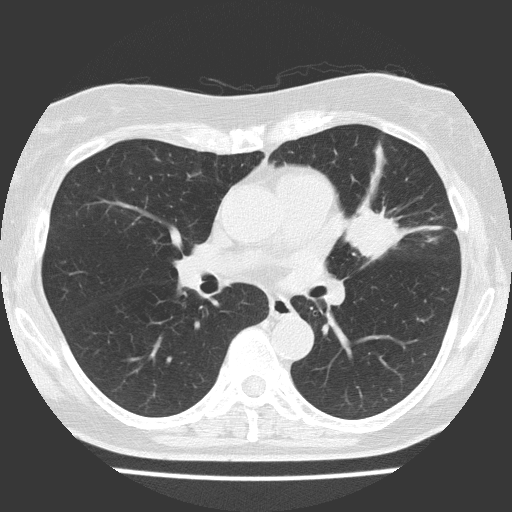
Low-dose screening chest CT, one axial slice. Position 81 of 151 along the scan axis. Reconstruction kernel FC51. 120 kVp. Lung window (W 1500 / L -600 HU). 2 mm slice thickness. 512 × 512 image matrix.
Annotated regions visible in this slice (outlined manually by an expert reader):
- lesion 1 (tumor, upper lobe of left lung): bounding box [x1, y1, x2, y2] px = [343, 202, 400, 258]